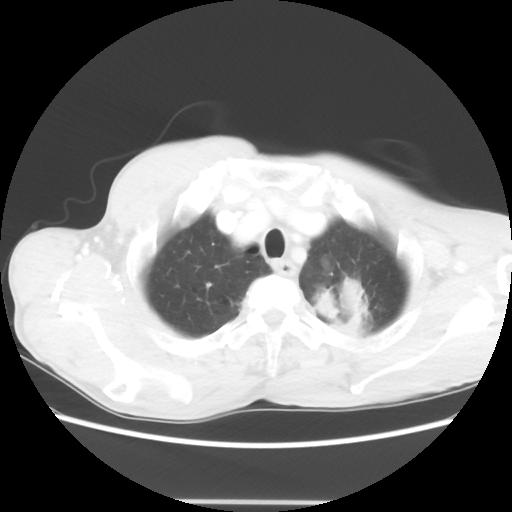
Chest CT, one axial slice. Slice 57 of 62 in the series (ordered by position). 100 kVp. Lung window (W 1500 / L -600 HU). 5 mm slice thickness. 512 × 512 image matrix, field of view 360 × 360 mm. Male patient, age 61 years. From the clinical record (not read from this slice): clinical TNM (as recorded): T3 N1 M1.
Outlined on this slice (bounding box drawn by a radiologist):
- lung tumour (recorded histology: adenocarcinoma): bounding box <310,273,371,336> (left, top, right, bottom; pixels)